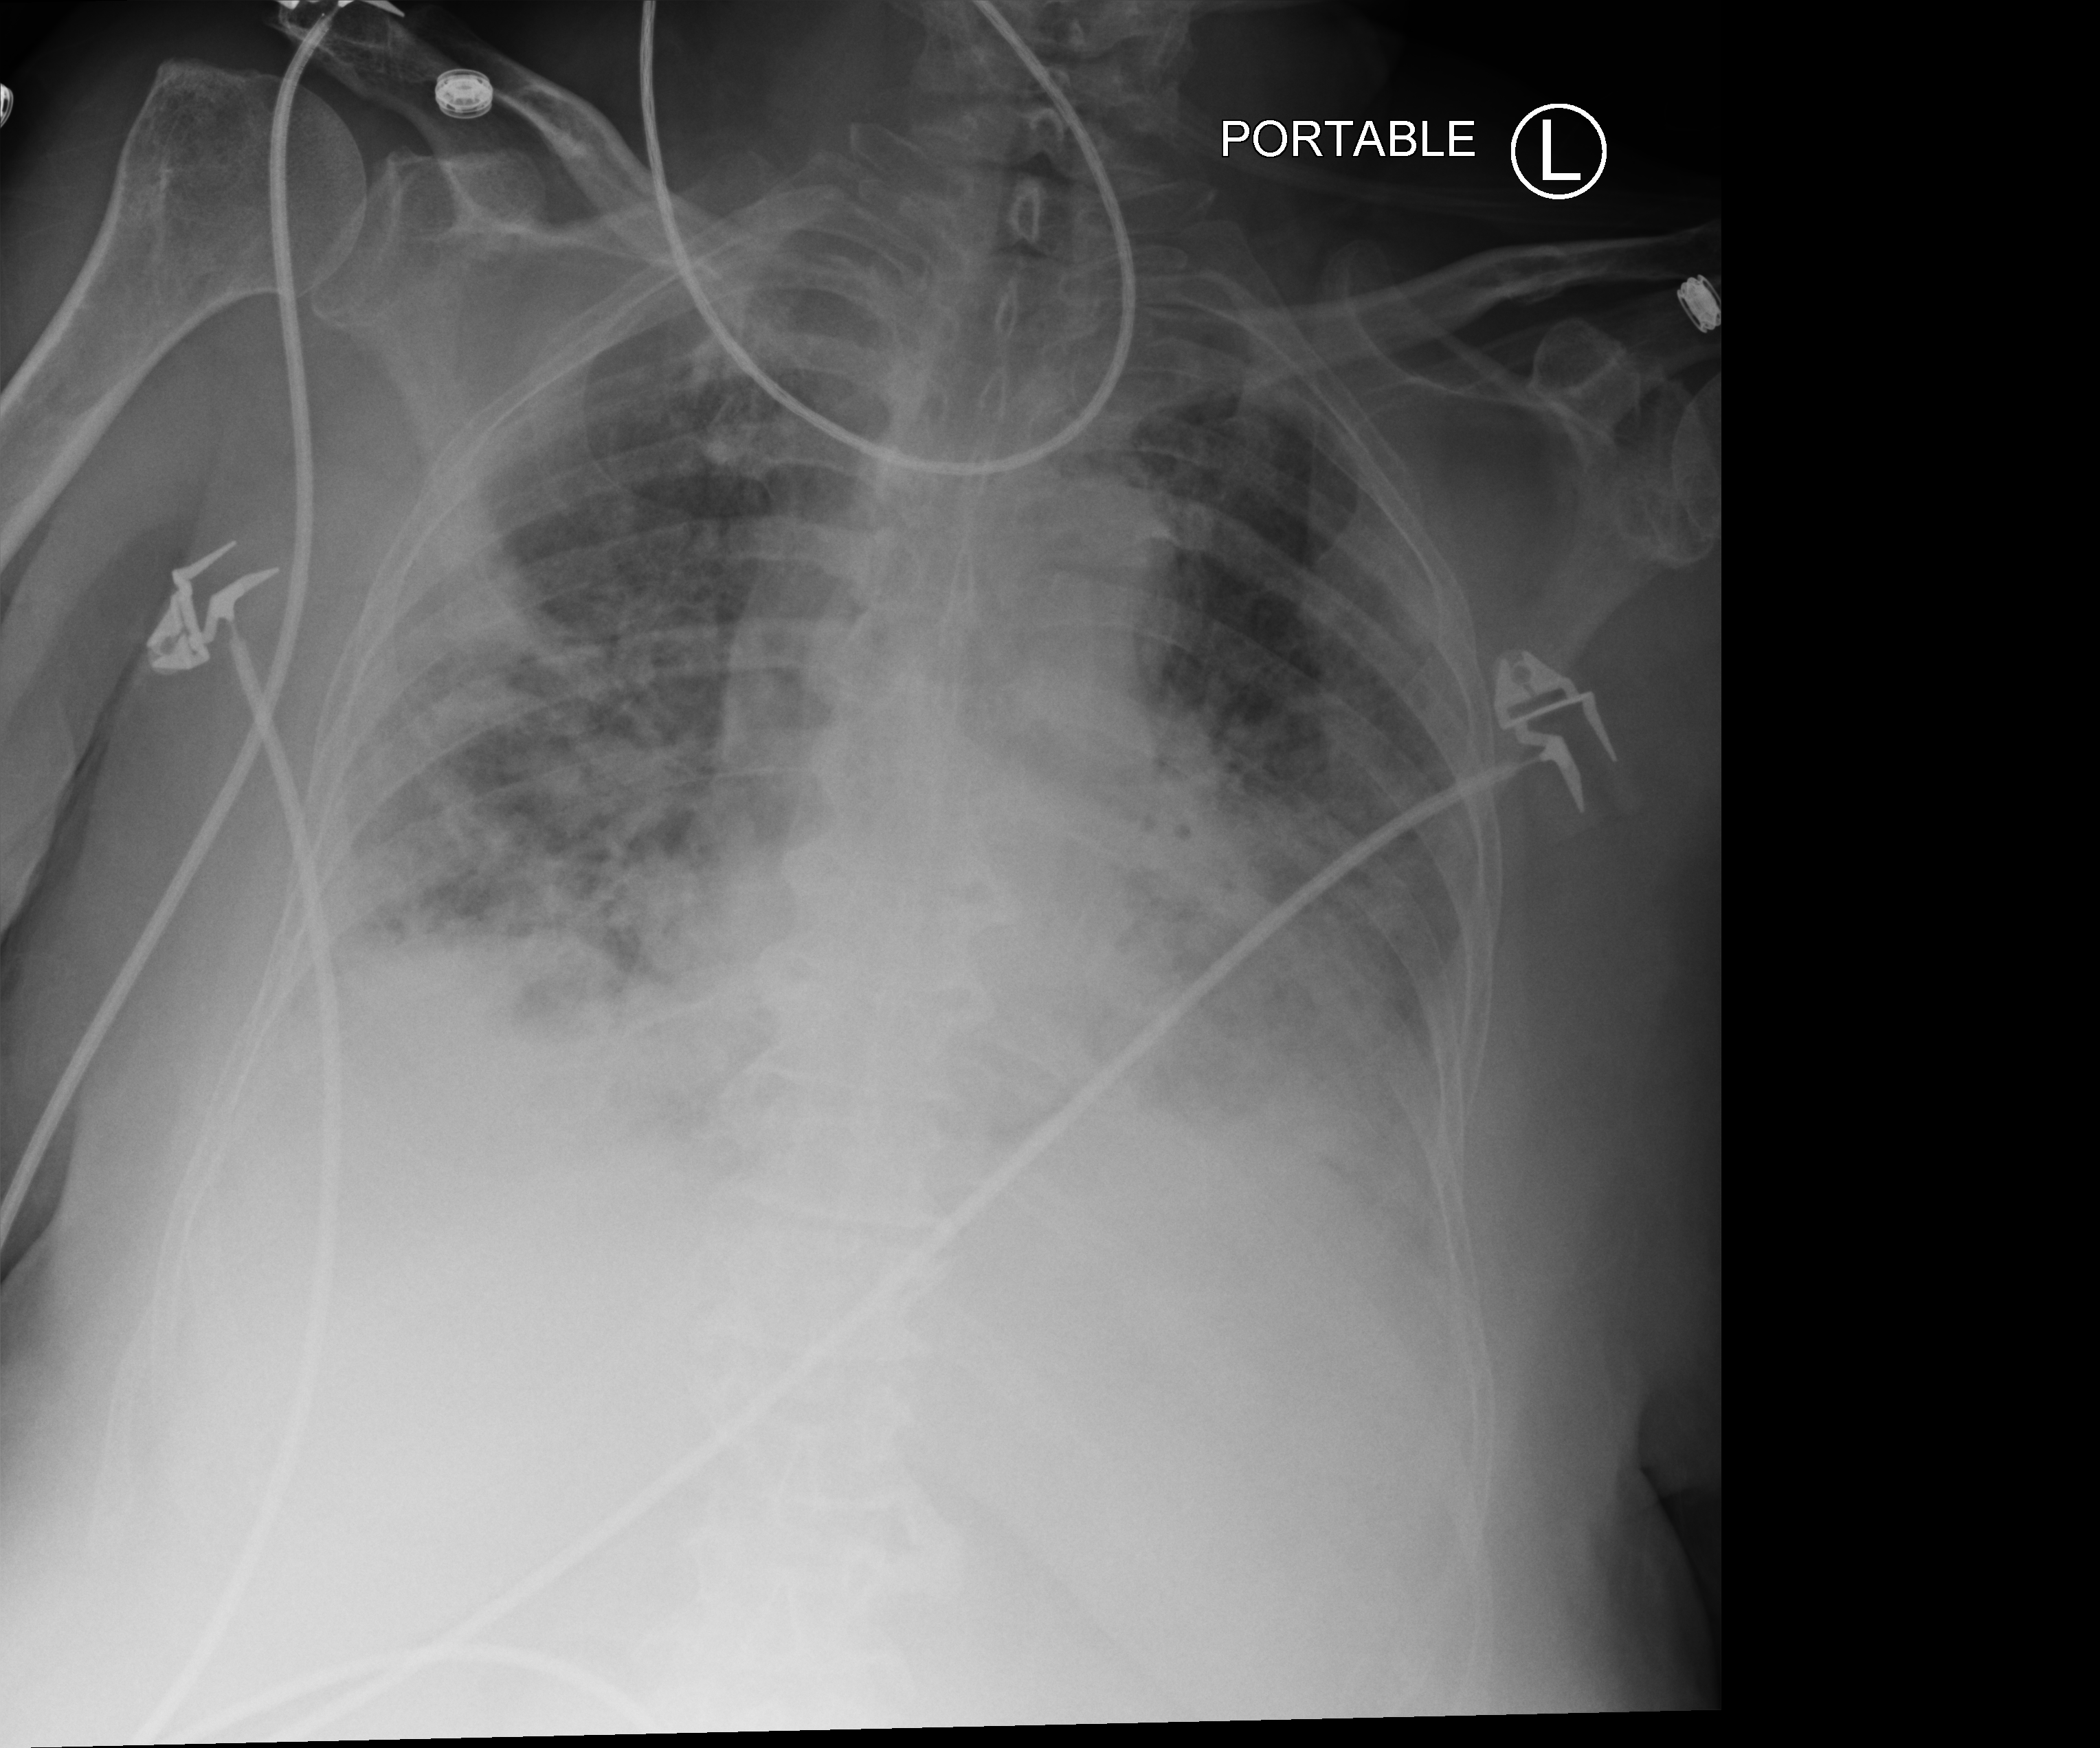
Portable chest radiograph, anteroposterior (AP) projection. Patient hospitalised with COVID-19; female, aged 75–90 years.
From the hospital-stay record, not from the radiograph (when in the stay this image was taken is not recorded): mechanically ventilated during this hospital stay: no; length of hospital stay: 37 days.